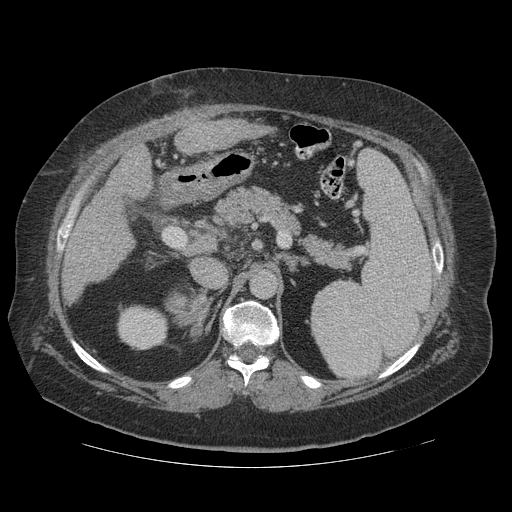
Contrast-enhanced abdominal CT (liver protocol), one axial slice. Position 65 of 121 along the scan axis. Reconstruction kernel STANDARD. Soft-tissue window (W 400 / L 40 HU). 512 × 512 image matrix, field of view 420 × 420 mm. From the clinical record (not read from this slice): diagnosis: hepatocellular carcinoma (patient treated with transarterial chemoembolisation; whether this scan precedes or follows treatment is not stated here); TNM stage (as recorded): Stage-IIIA; Child-Pugh class: A.
Outlined on this slice (semi-automatic segmentation, software-assisted and operator-edited):
- liver parenchyma outside the tumour (the mass and vessels are separate outlines, so this box may not span the whole liver): bounding box (x1, y1, x2, y2) in pixels: (88, 120, 268, 230)
- liver vessels: (135, 162, 138, 164)